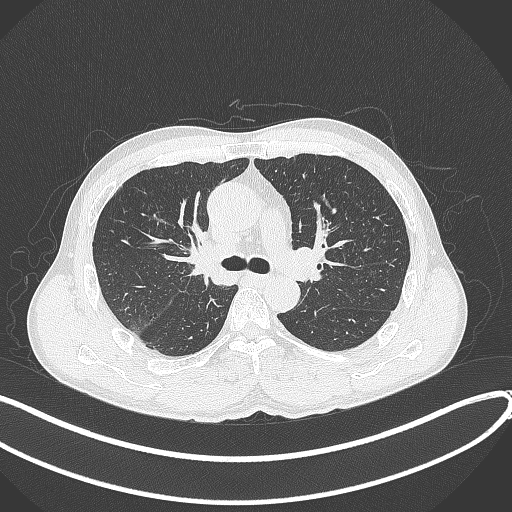
Chest CT, one axial slice; slice 245 of 409 in the series (ordered by position); reconstruction kernel B70f; 120 kVp; lung window (W 1500 / L -600 HU); 1 mm slice thickness; 512 × 512 image matrix, field of view 400 × 400 mm. Male patient, age 53 years. Case-level facts recorded for this patient, not image findings: clinical TNM (as recorded): T1b N0 M0.
Annotated regions visible in this slice (bounding box drawn by a radiologist):
- lung tumour (recorded histology: squamous cell carcinoma): bounding box (x1, y1, x2, y2) in pixels: (180, 219, 233, 287)